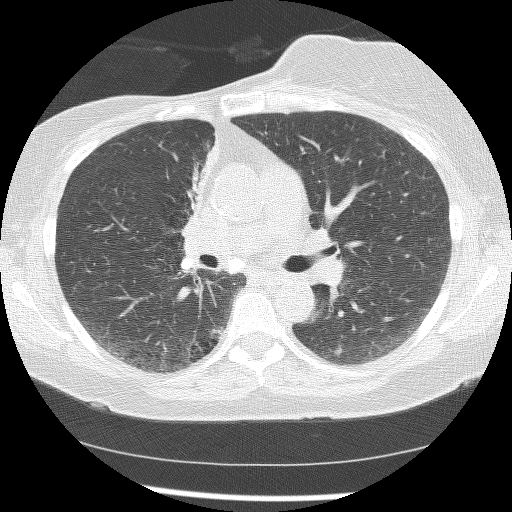
Axial slice from a low-dose chest CT screening exam; baseline screening round; lung window (W 1500 / L -600 HU). Female, age 56 years at enrolment.
Expert-annotated lung lesion, box from (x=160, y=135) to (x=214, y=254) px. The screening reader recorded 2 non-calcified nodules or masses ≥4 mm on this exam; which of them this box marks is not recorded. Later outcome: lung cancer diagnosed 1185 days after this screen (after the third annual screen) — adenocarcinoma, NOS, right upper lobe, stage IIIB (AJCC 6th edition), 8 mm at pathology.